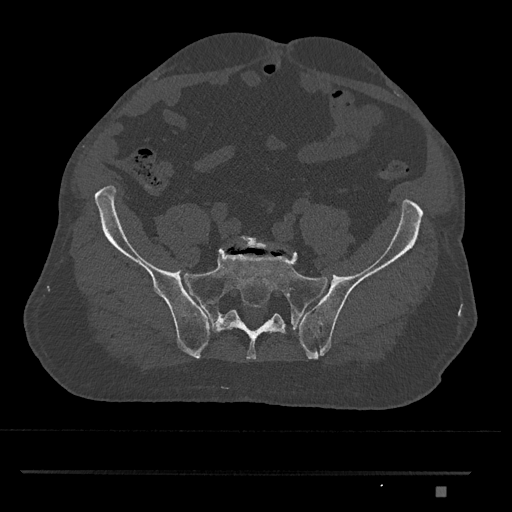
CT including the spine, one axial slice; slice 494 of 1134 in the series (ordered by position); bone window (W 1800 / L 400 HU); 0.5 mm slice thickness; 512 × 512 image matrix, field of view 429 × 429 mm. Male patient, age 65 years. Case-level facts recorded for this patient, not image findings: primary cancer: prostate.
Structures marked on this image (semi-automatically segmented with operator editing):
- L5 vertebra: box from (x=237, y=236) to (x=279, y=249) px